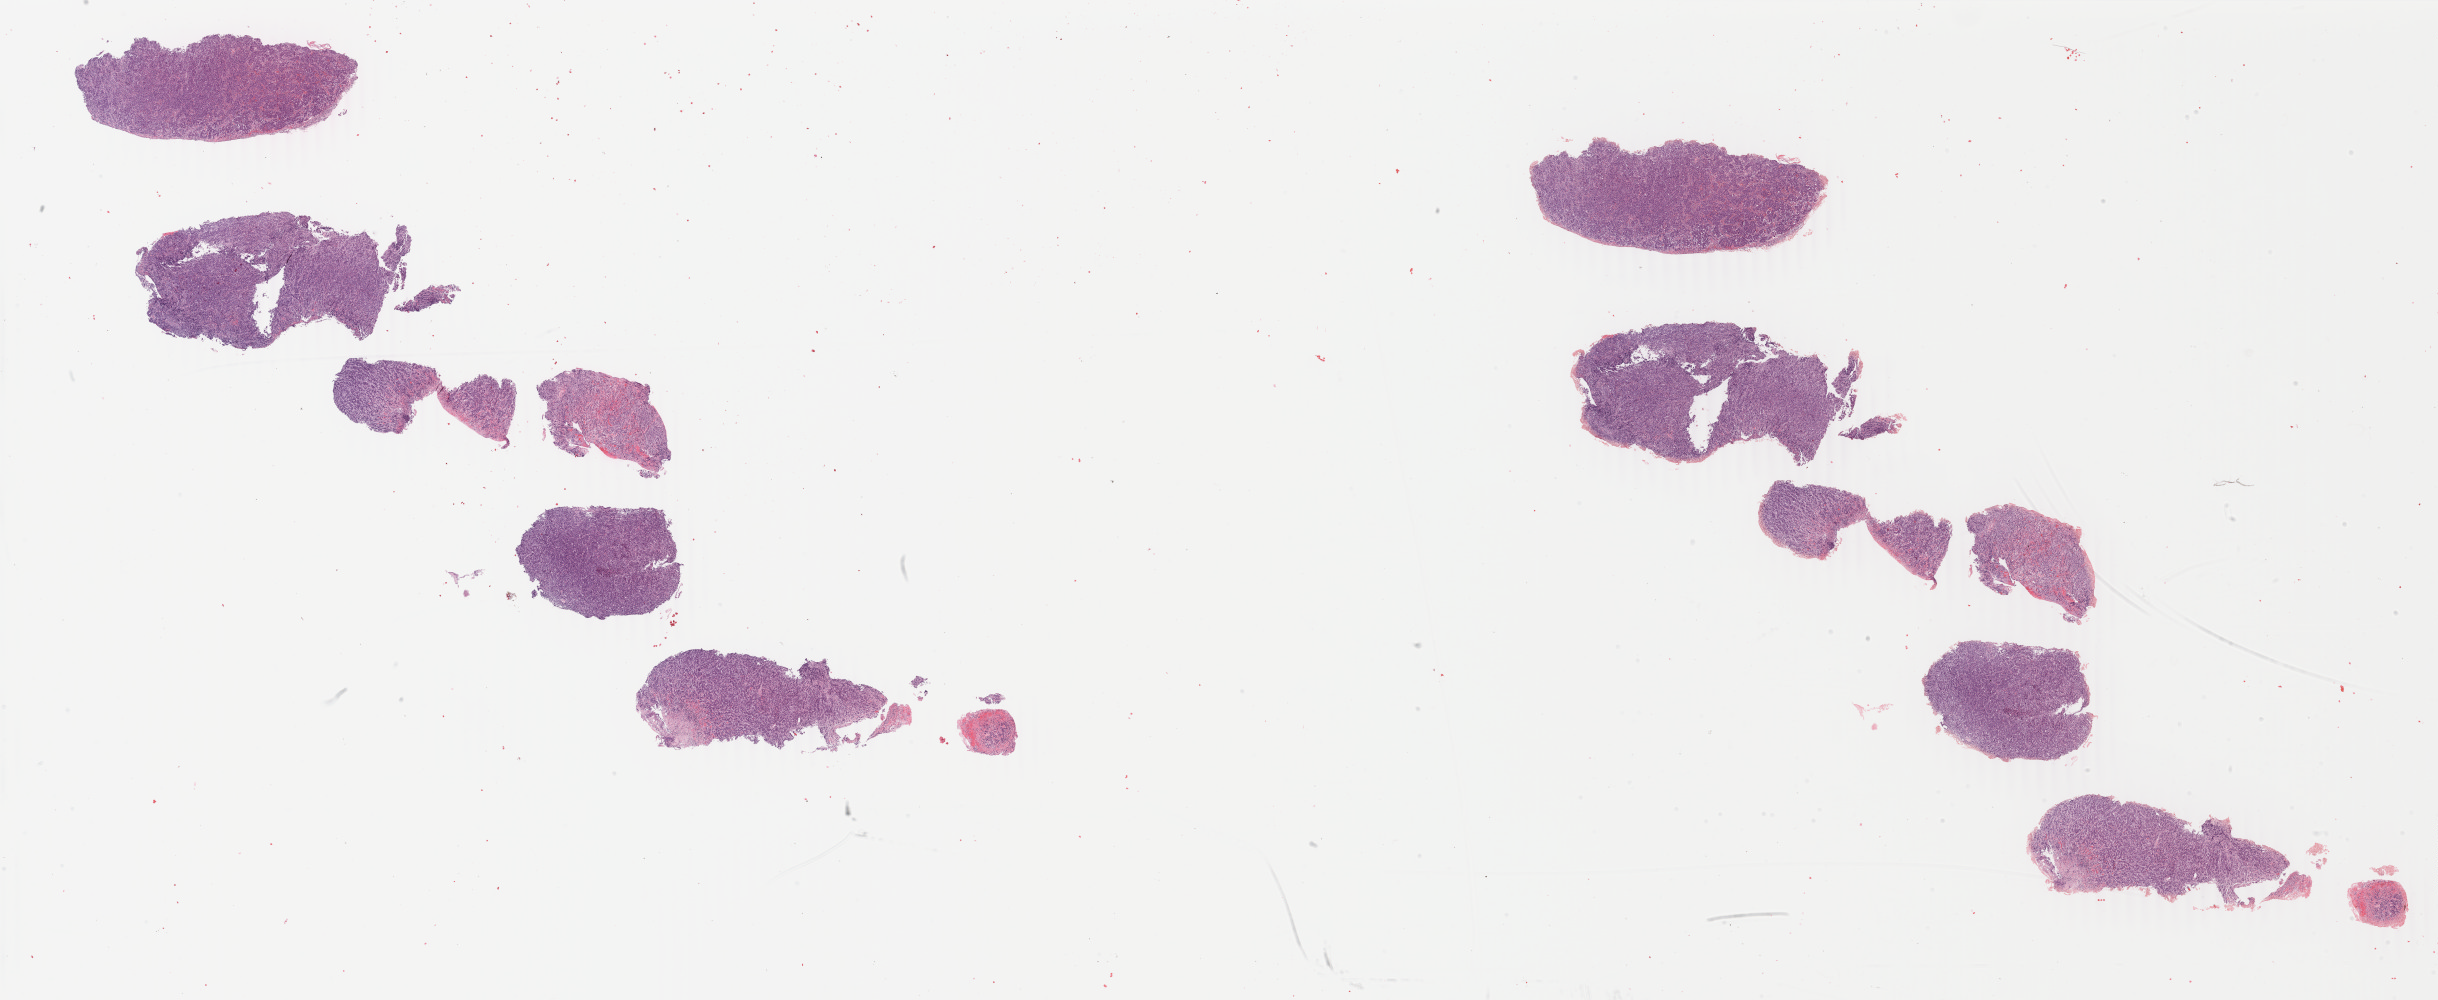
Whole-slide histology image, H&E, whole scanned area (about 38.8 x 15.9 mm, acquisition: 40x scan) shown as a low-resolution overview; FFPE section; sample: primary tumour, stomach. Patient: female, age at initial diagnosis 44 years.
Pathologic diagnosis: Carcinoma, diffuse type.